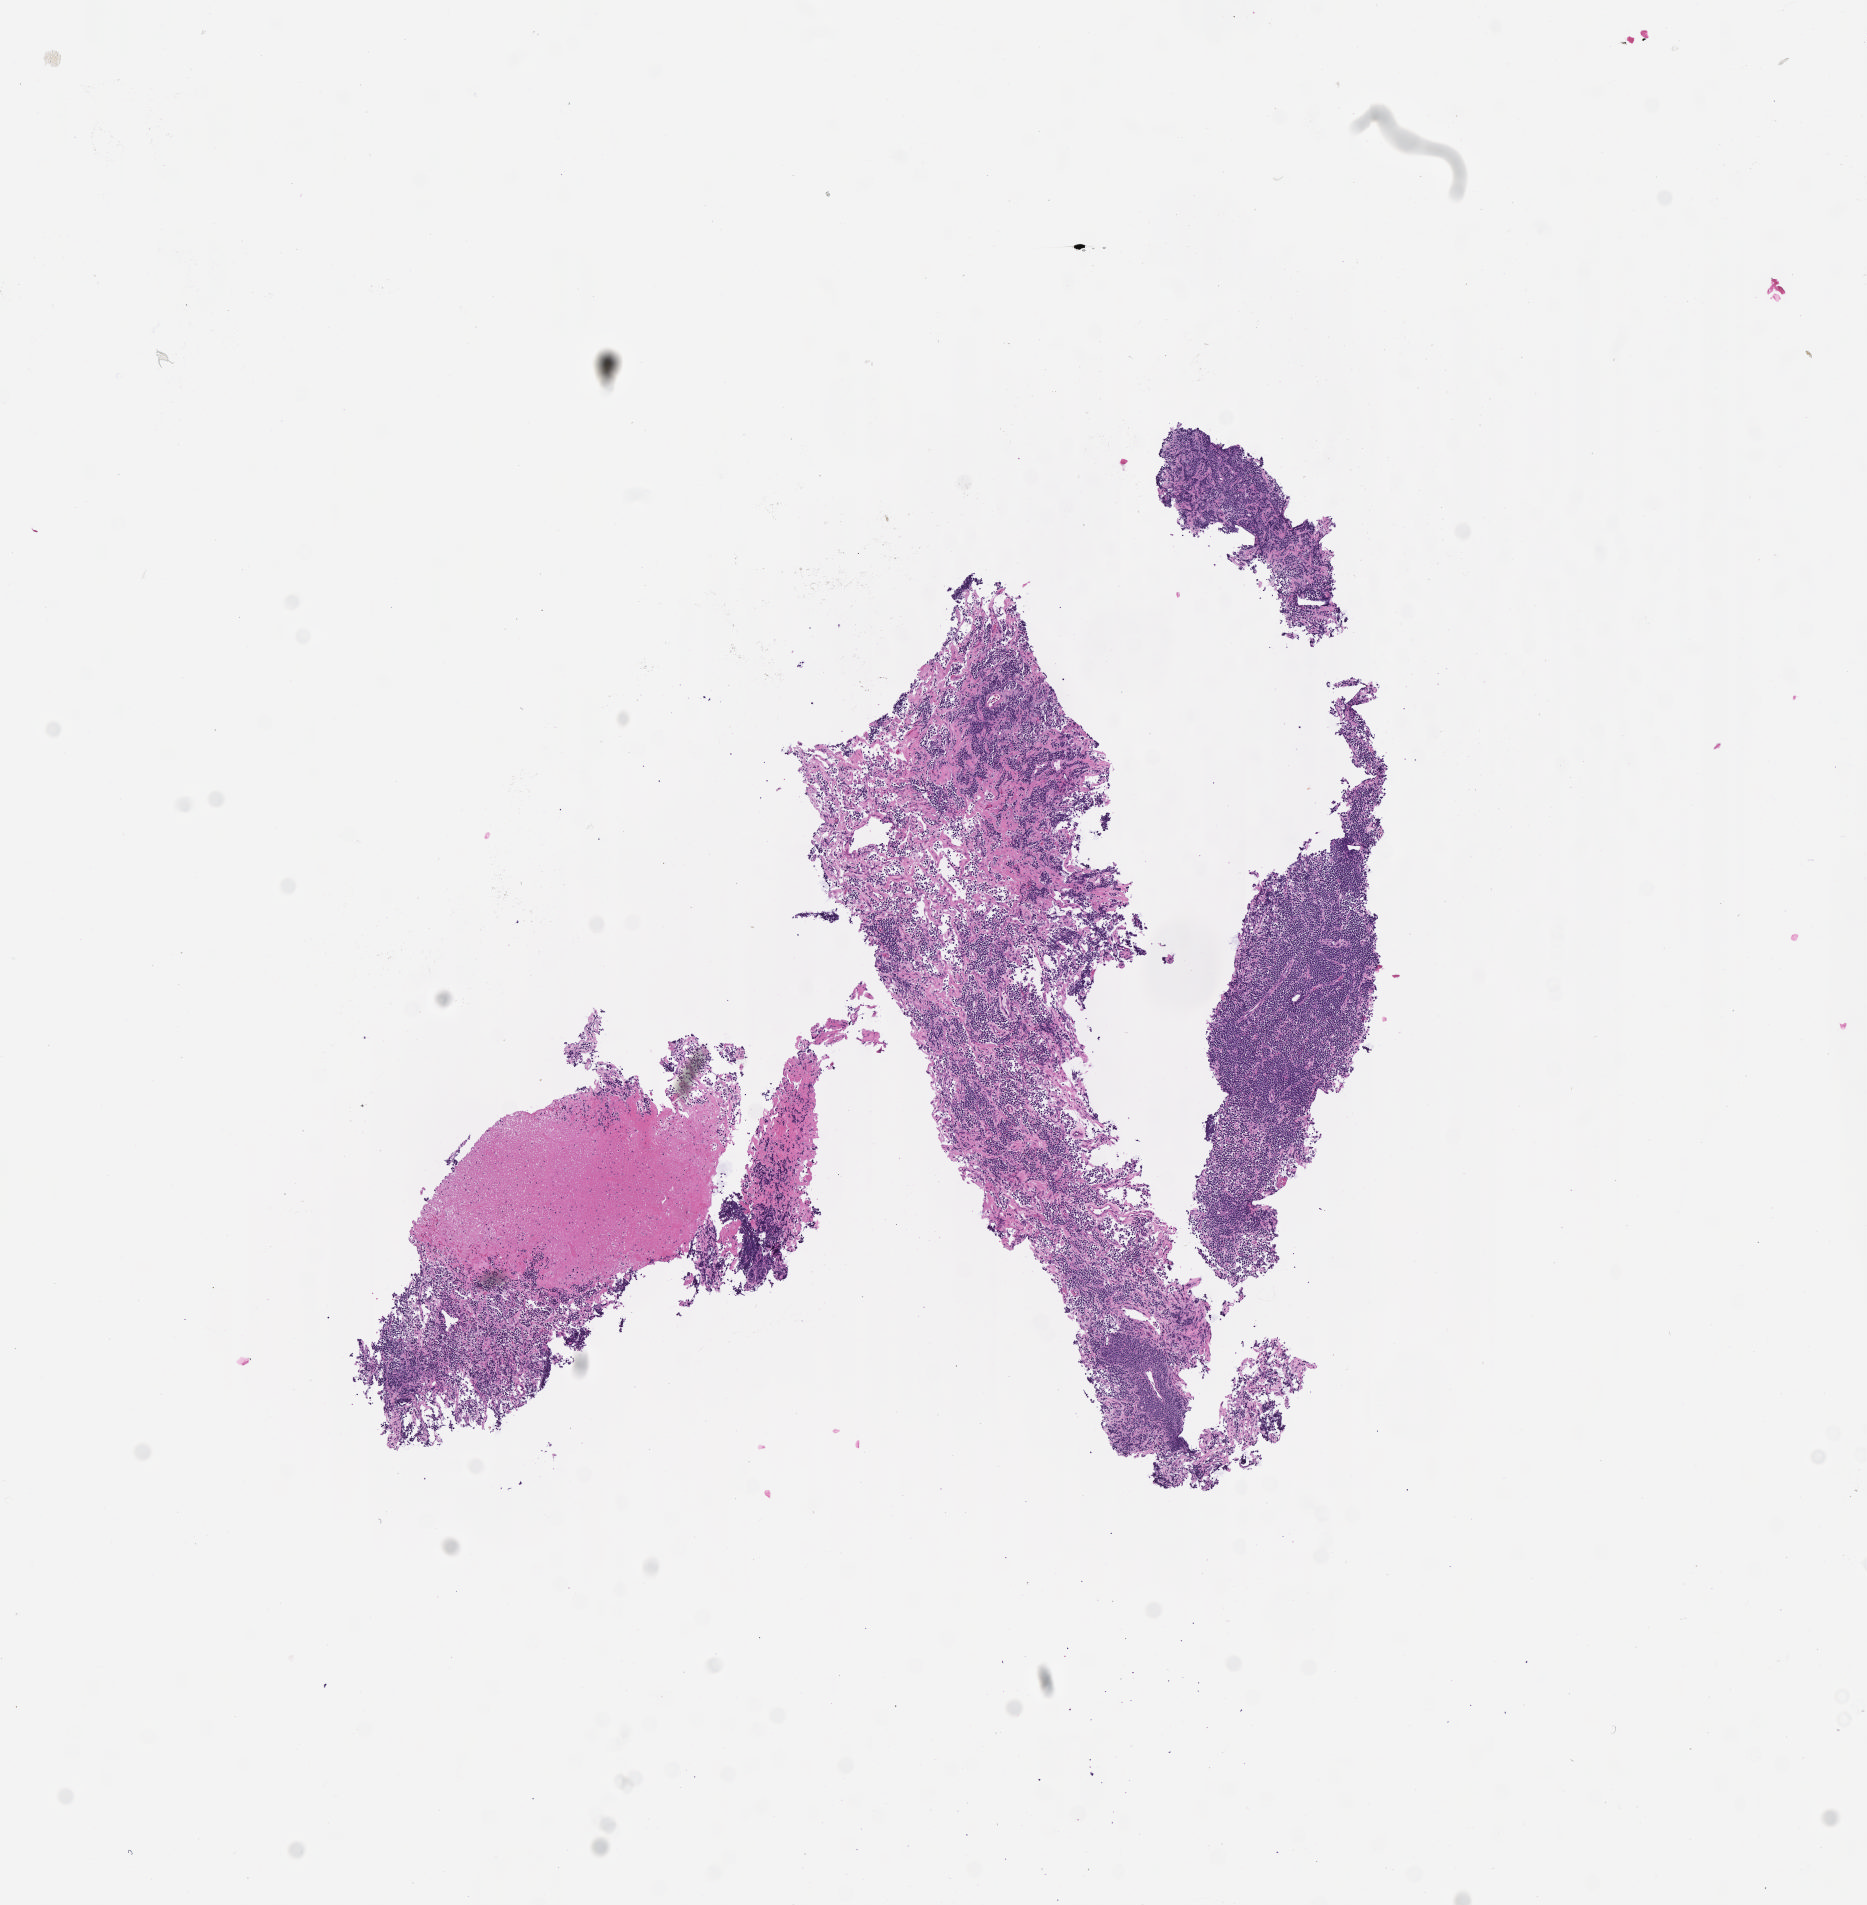
Whole-slide image, haematoxylin and eosin stain — whole scanned area (about 7.5 x 7.7 mm) shown as a low-resolution overview. Specimen: tumor tissue. Site: pelvis. Patient: female, age at initial diagnosis 7 years.
• diagnosis: Burkitt lymphoma, NOS